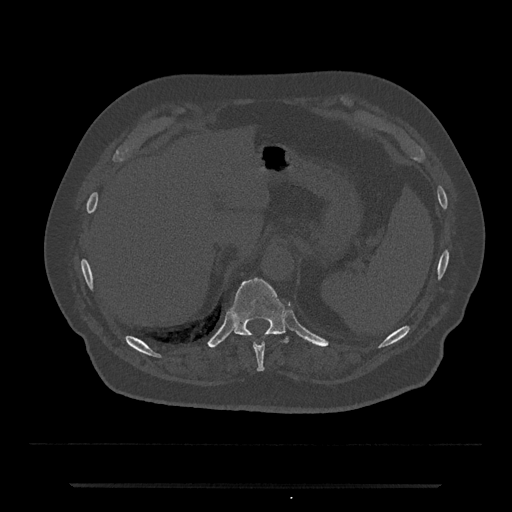
CT including the spine, one axial slice; position 671 of 797 along the scan axis; bone window (W 1800 / L 400 HU); 512 × 512 image matrix, field of view 434 × 434 mm. Male patient, age 80 years. From the clinical record (not read from this slice): primary cancer: prostate.
Outlined on this slice (semi-automatically segmented with operator editing):
- T10 vertebra: bounding box [x1, y1, x2, y2] px = [253, 343, 265, 371]
- T11 vertebra: [230, 278, 290, 343]